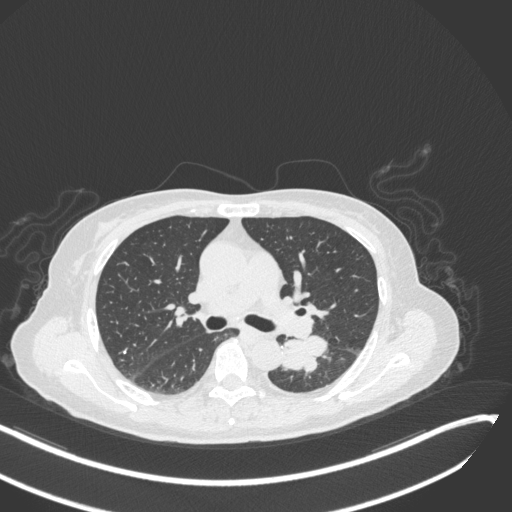
Chest CT, one axial slice; slice 171 of 342 in the series (ordered by position); lung window (W 1500 / L -600 HU); 512 × 512 image matrix. Female patient, age 64 years. Case-level facts recorded for this patient, not image findings: clinical TNM (as recorded): T3 N1 M1; histopathological grade: G3.
Annotated regions visible in this slice (rectangle marked by the reading radiologist):
- lung tumour (recorded histology: small cell carcinoma): bounding box (x1, y1, x2, y2) in pixels: (275, 334, 332, 376)